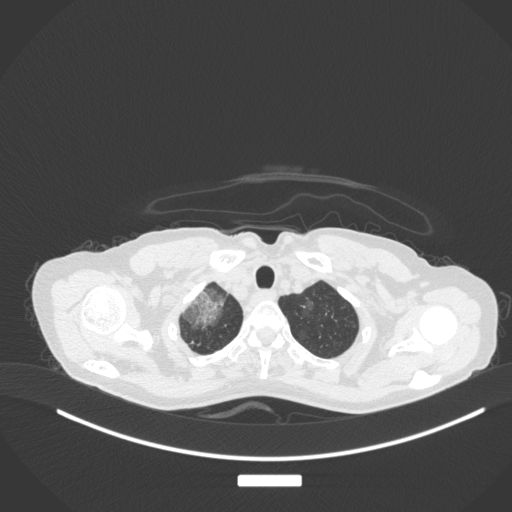
Chest CT, one axial slice; slice 300 of 311 in the series (ordered by position); reconstruction kernel B31f; 120 kVp; lung window (W 1500 / L -600 HU); 1 mm slice thickness; 512 × 512 image matrix, field of view 400 × 400 mm. Female patient, age 59 years. Case-level facts recorded for this patient, not image findings: clinical TNM (as recorded): T3 N0 M0.
Annotated regions visible in this slice (bounding box drawn by a radiologist):
- lung tumour (recorded histology: adenocarcinoma): bounding box (x1, y1, x2, y2) in pixels: (178, 284, 226, 328)